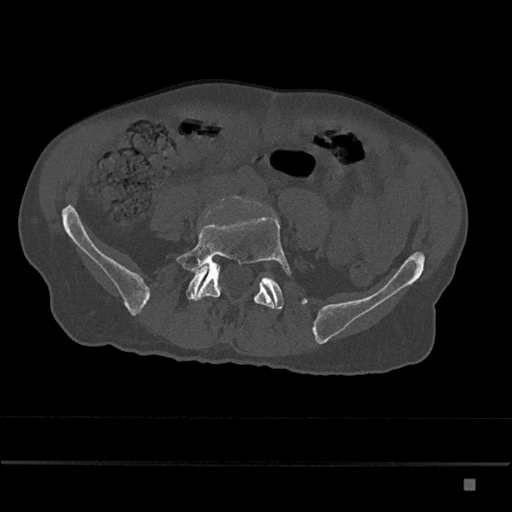
CT including the spine, one axial slice. Position 274 of 797 along the scan axis. Reconstruction kernel Br40s/3. Bone window (W 1800 / L 400 HU). 0.5 mm slice thickness. 512 × 512 image matrix, field of view 390 × 390 mm. Patient: male, 72 years. Case-level facts recorded for this patient, not image findings: primary cancer: prostate.
Annotated regions visible in this slice (semi-automatically segmented with operator editing):
- L5 vertebra: box from (x=176, y=203) to (x=292, y=309) px